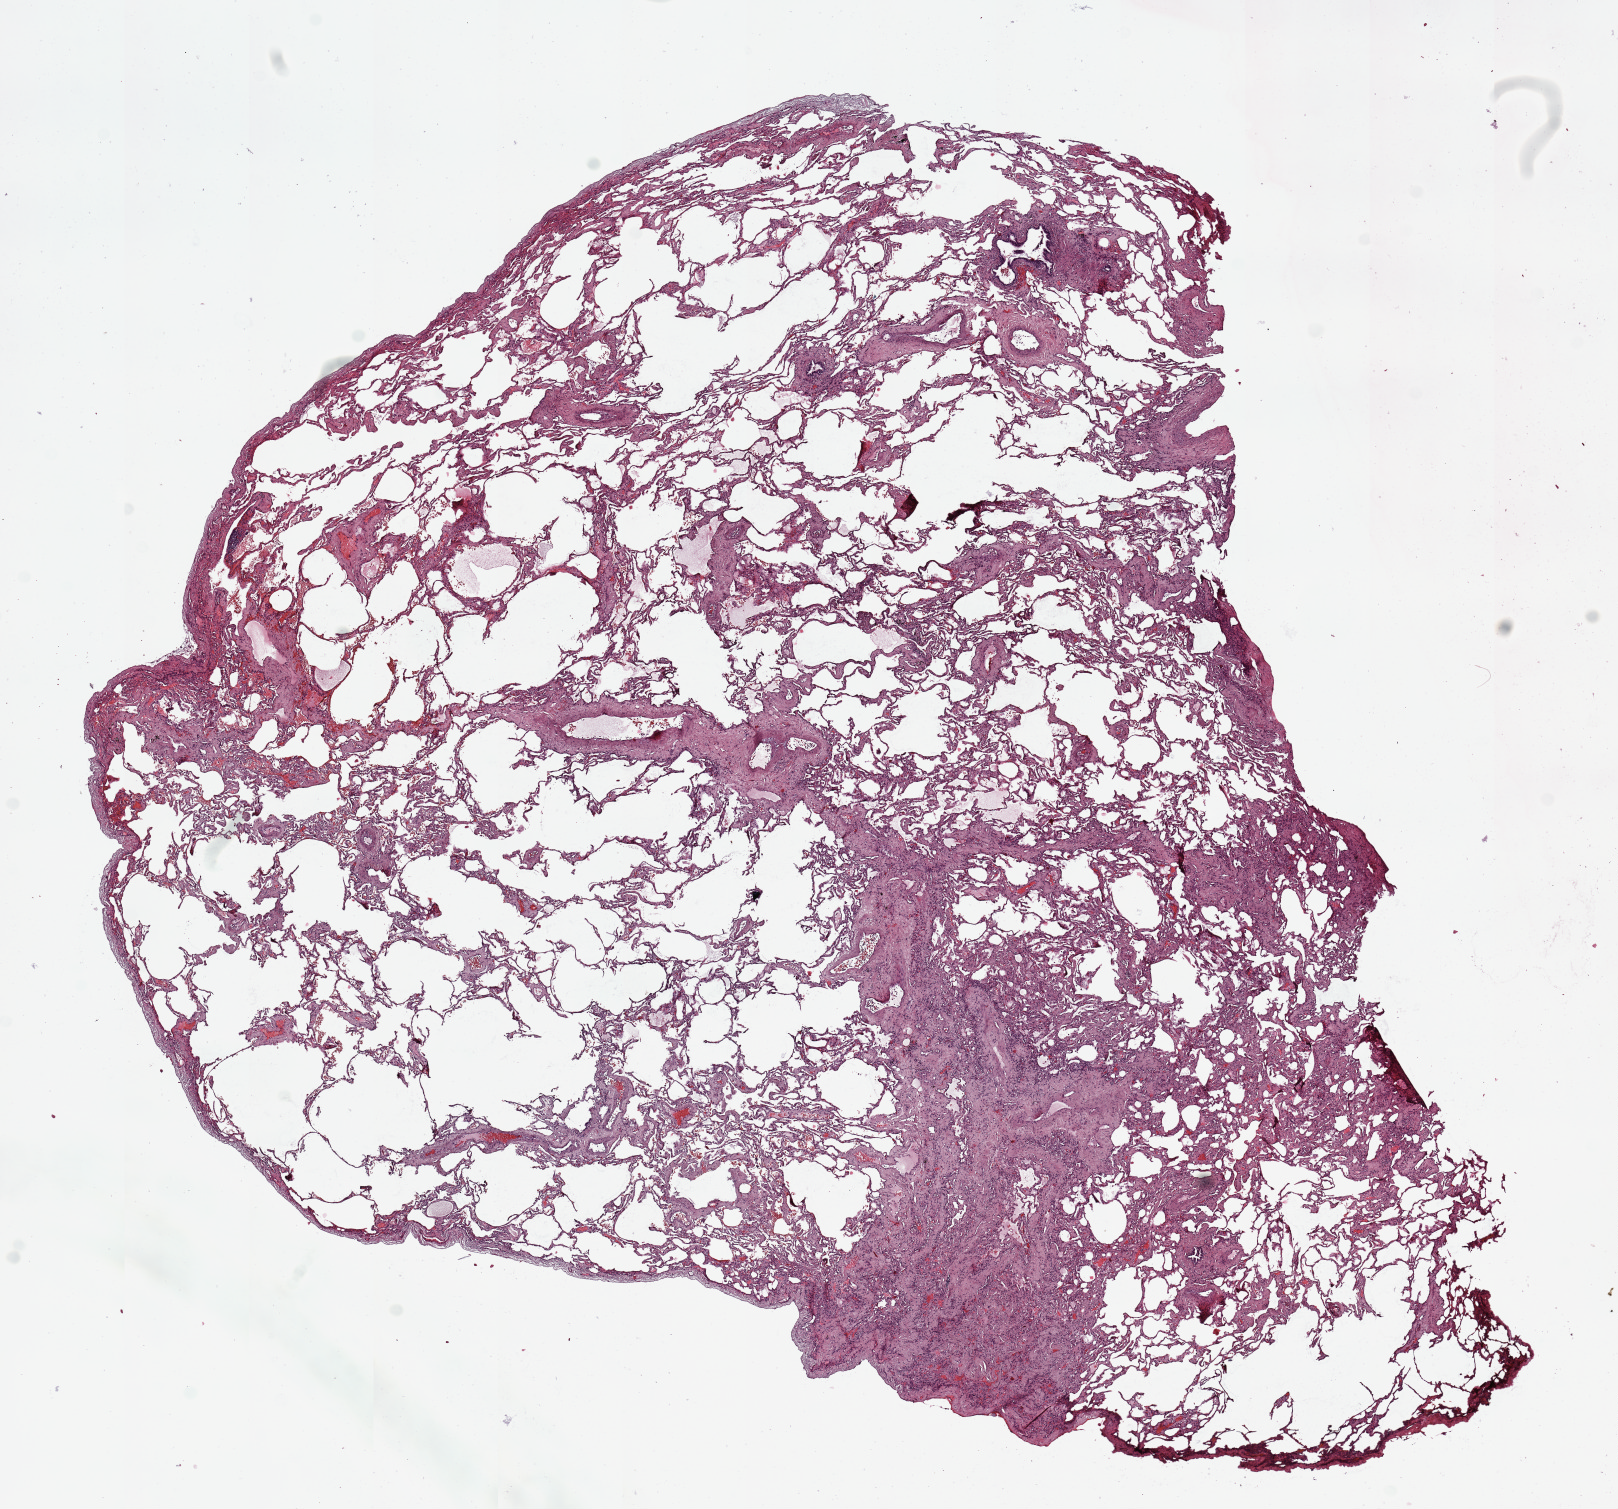
Hematoxylin and eosin (H&E) stained whole-slide image, whole scanned area (about 12.8 x 11.9 mm, slide scanned at 20x) shown as a low-resolution overview, normal (non-tumour) tissue sample, sampled site: lung. 58-year-old male patient.
- this section: normal (non-tumour) tissue from the same patient
- patient diagnosis: Squamous cell carcinoma, NOS